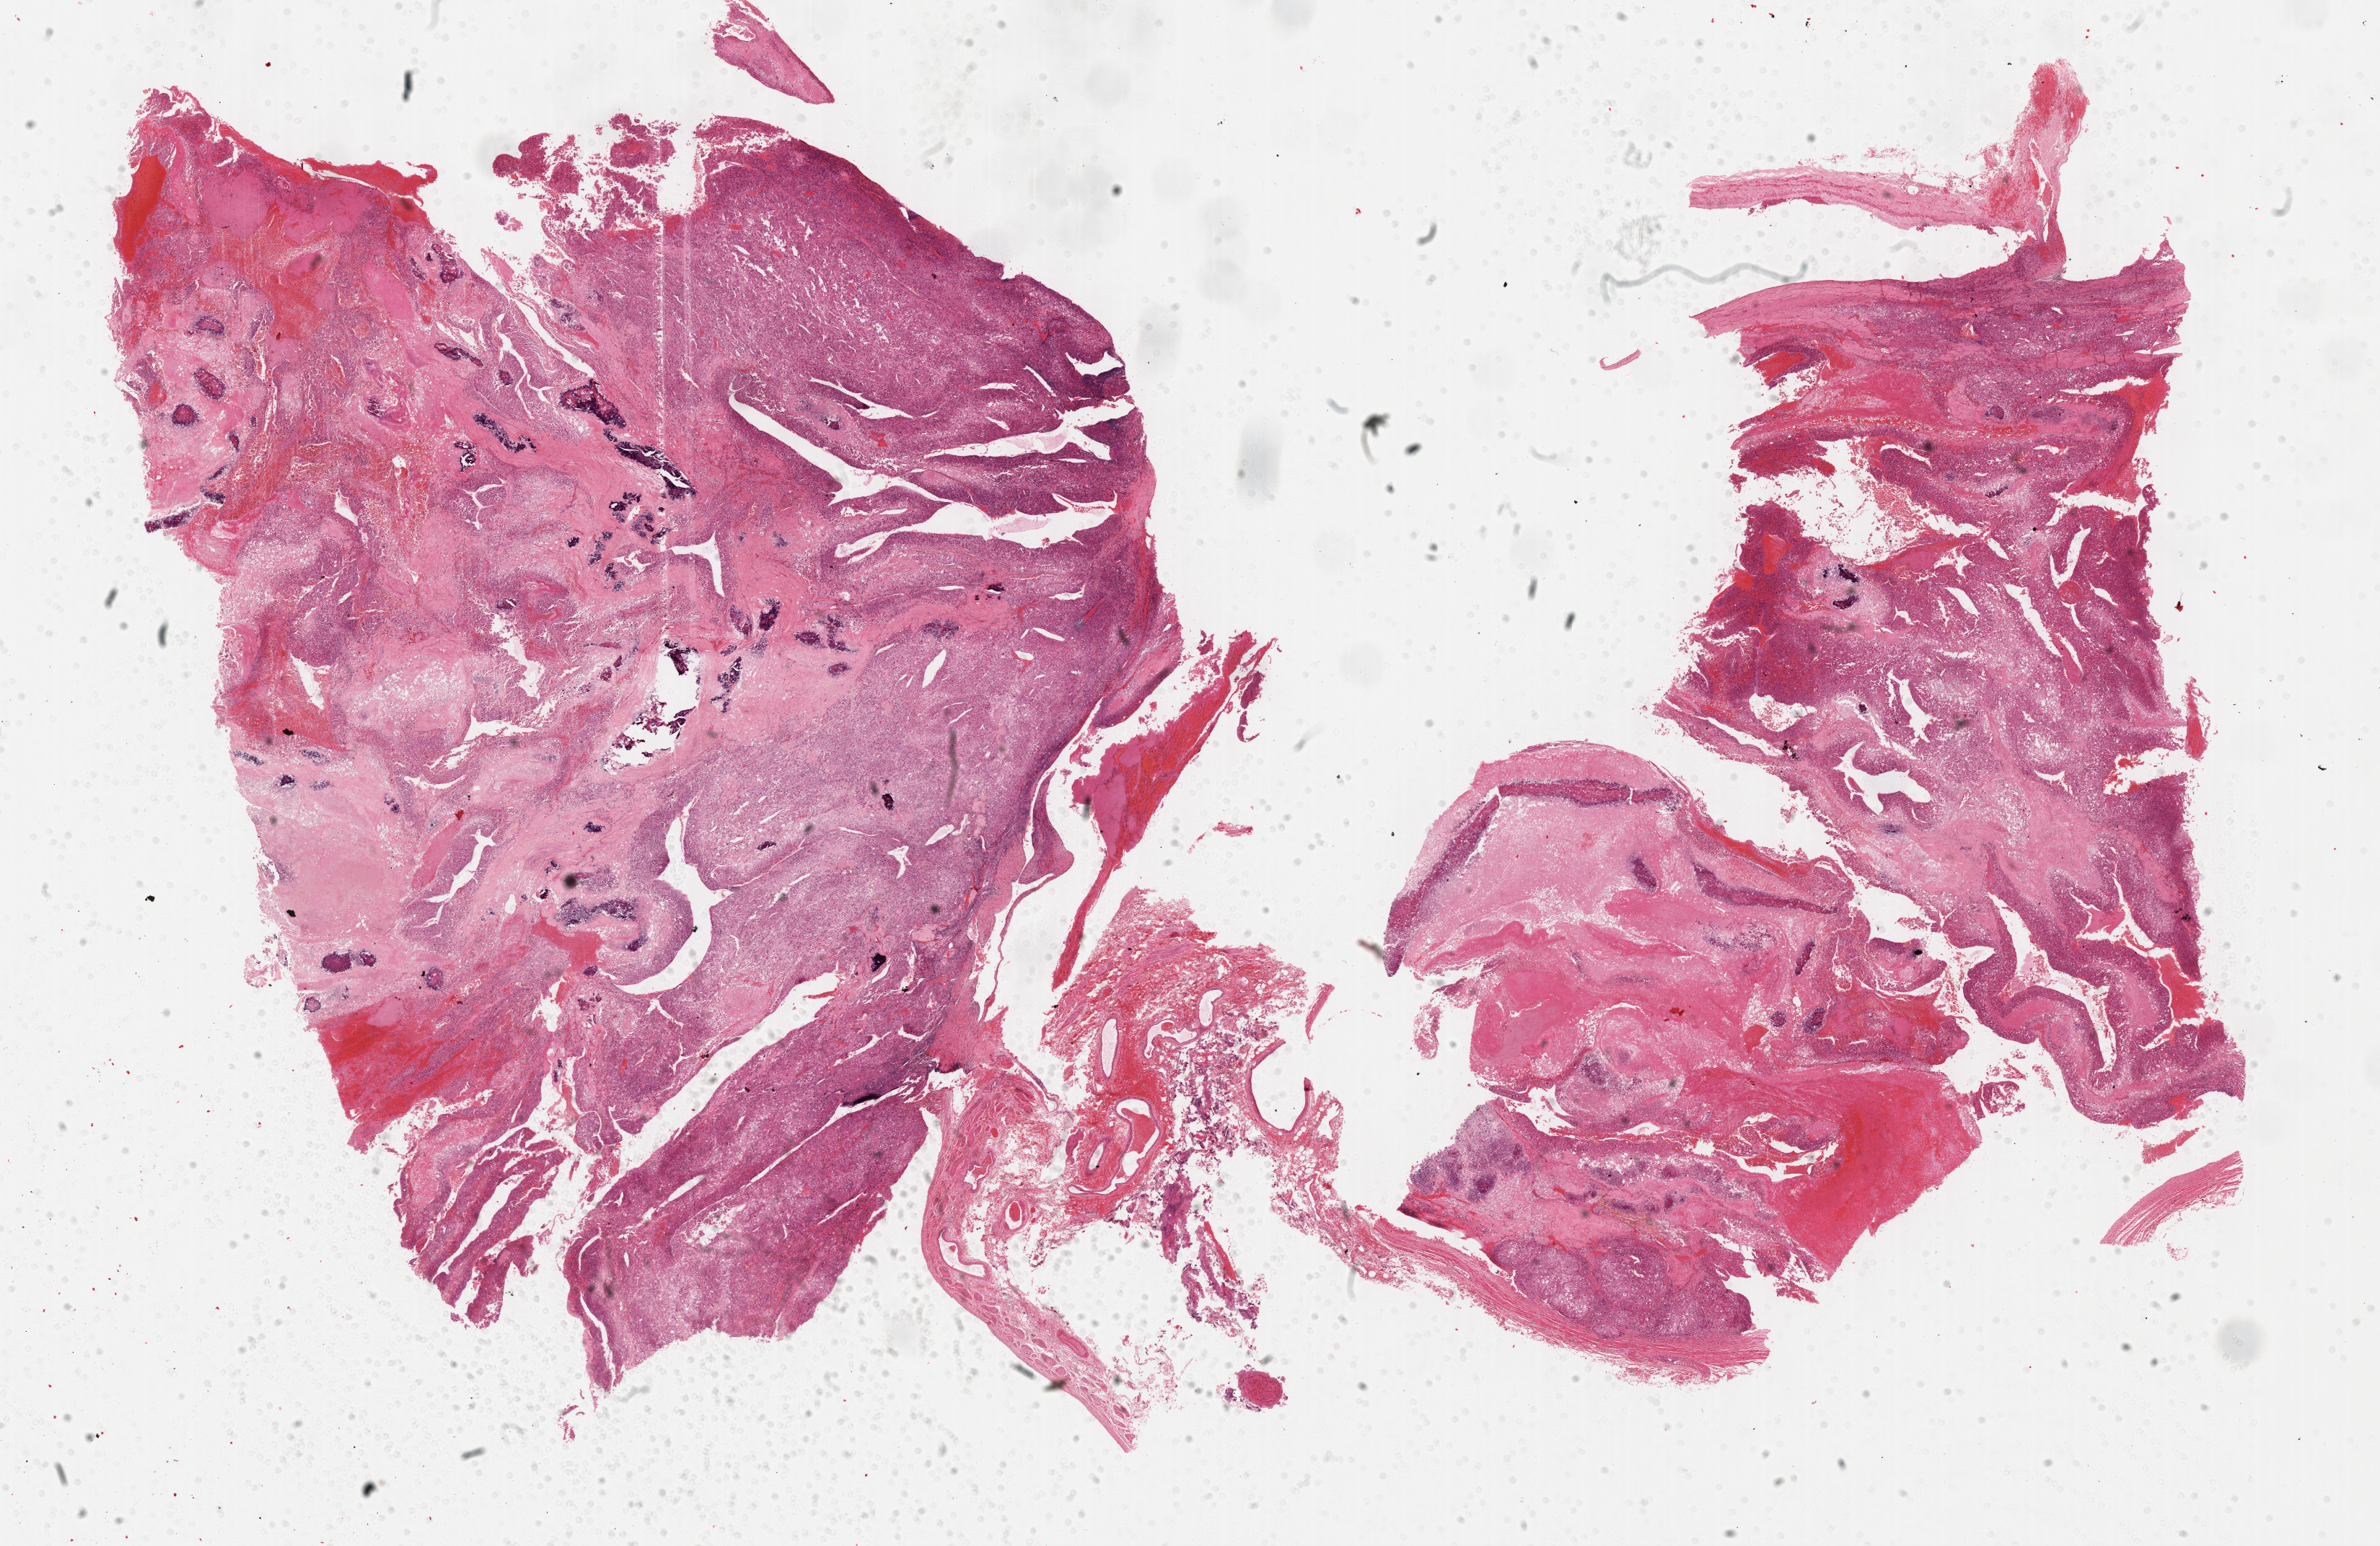
H&E-stained whole-slide image, shown as a low-resolution overview of the whole scanned area (about 26.7 x 17.3 mm, acquisition: 40x scan). Formalin-fixed paraffin-embedded (FFPE) diagnostic section. Sample: primary tumour, adrenal cortex. Male, age 49 years at initial diagnosis.
- diagnosis: Adrenal cortical carcinoma (cortex of adrenal gland)